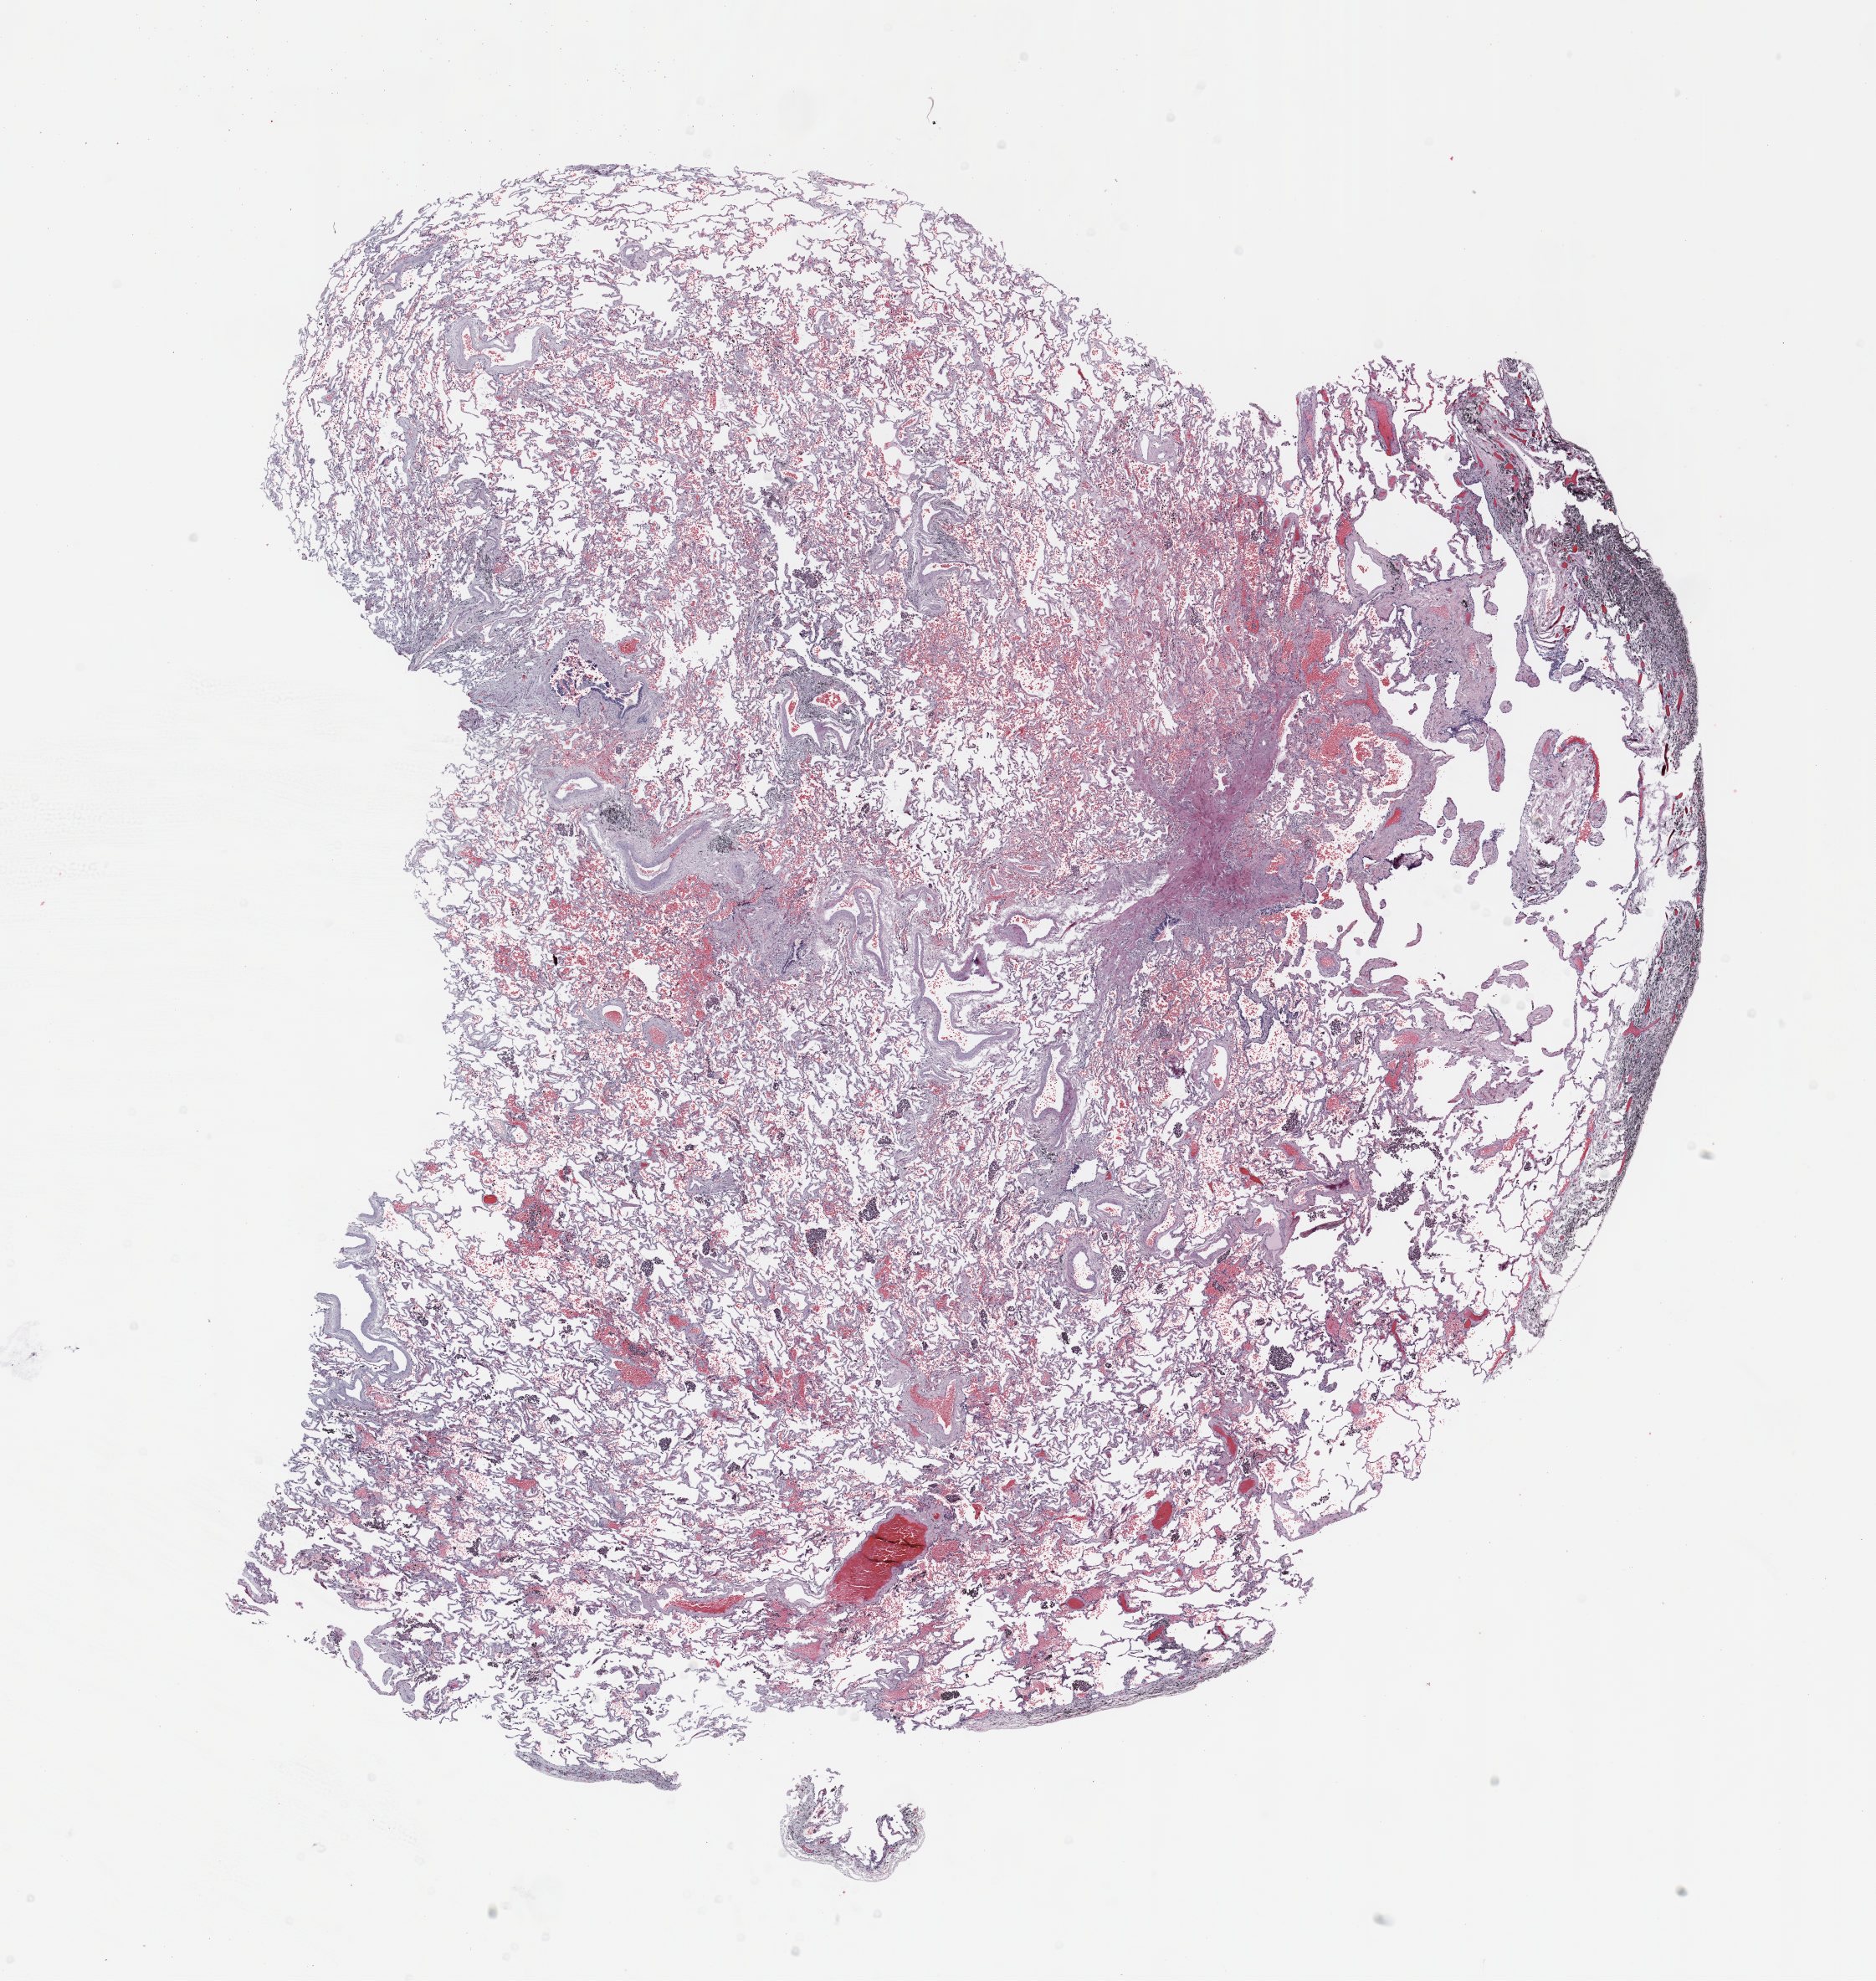
Whole-slide histology image, H&E, low-resolution overview of the scanned area, about 18.0 x 19.0 mm (slide scanned at 20x), FFPE section, lung. Male patient, aged 63 at enrolment. Current smoker at enrolment. Grade: moderately differentiated (G2).
- primary tumour location (clinical record): right upper lobe
- stage (AJCC 6th edition): IA
- participant's lung-cancer diagnosis: Bronchiolo-alveolar adenocarcinoma, NOS (ICD-O-3 8250/3)
- tumour size (pathology): 15 mm